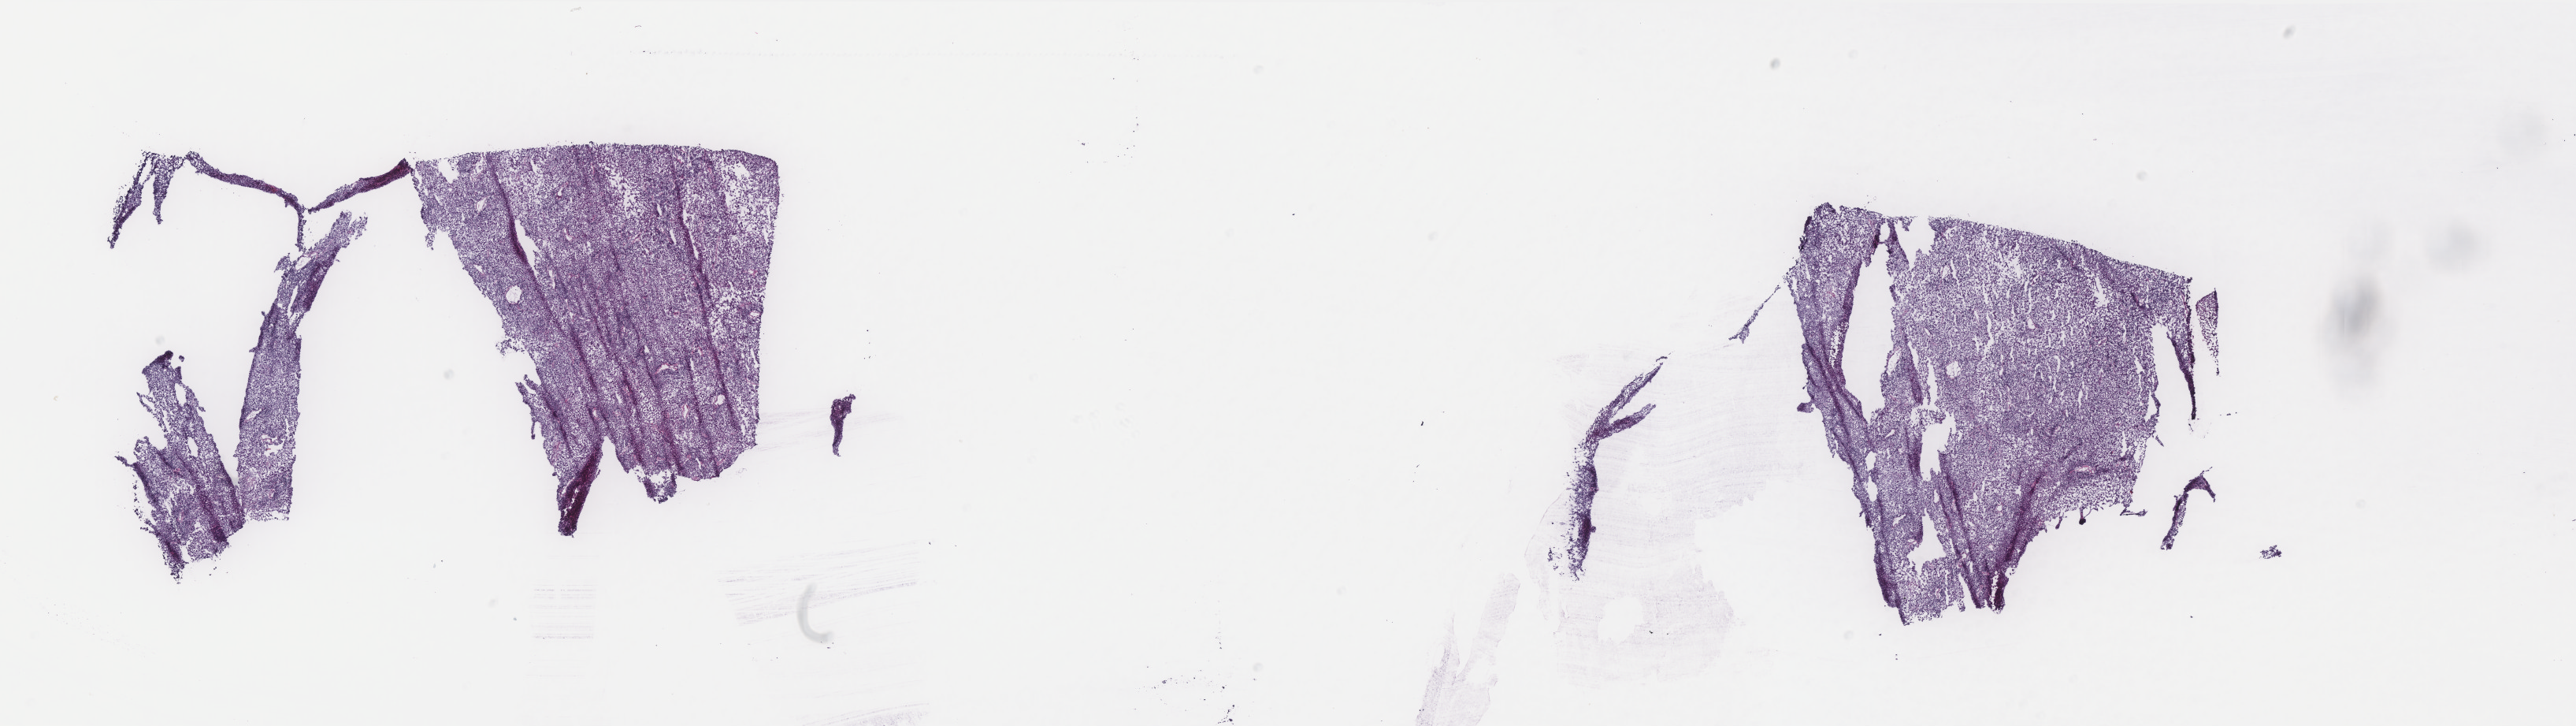
Digitized H&E tissue section (whole slide) — whole scanned area (about 26.2 x 7.4 mm, acquisition: 40x scan) shown as a low-resolution overview. Frozen section from the top of the tissue portion. Metastatic tumour sample, sampled site: skin of trunk. Patient: female, age at initial diagnosis 81 years. Pathologist review of this section (percent, as recorded): tumour cells 100%, tumour nuclei 90%, normal cells 0%, stromal cells 0%, necrosis 0%. Inflammatory infiltration, as recorded: lymphocyte infiltration 0%, monocyte infiltration 0%, neutrophil infiltration 0%.
This section: metastatic tumour tissue. Patient diagnosis: Malignant melanoma, NOS.